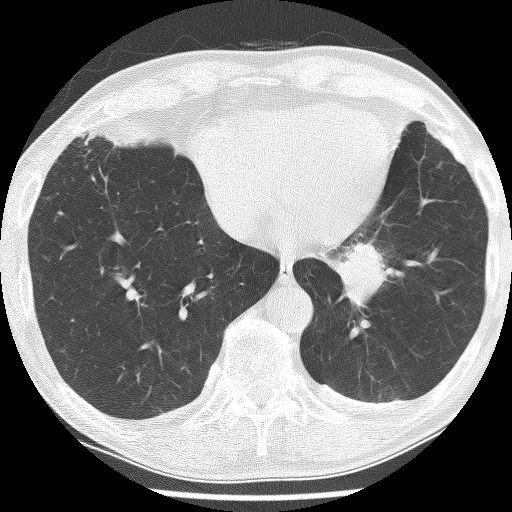
Low-dose screening chest CT, one axial slice; position 53 of 226 along the scan axis; reconstruction kernel BONE; lung window (W 1500 / L -600 HU); 2.5 mm slice thickness; 512 × 512 image matrix, field of view 320 × 320 mm.
Annotated regions visible in this slice (manually delineated by an expert):
- lesion 1 (tumor, lower lobe of left lung): box from (x=339, y=242) to (x=386, y=306) px